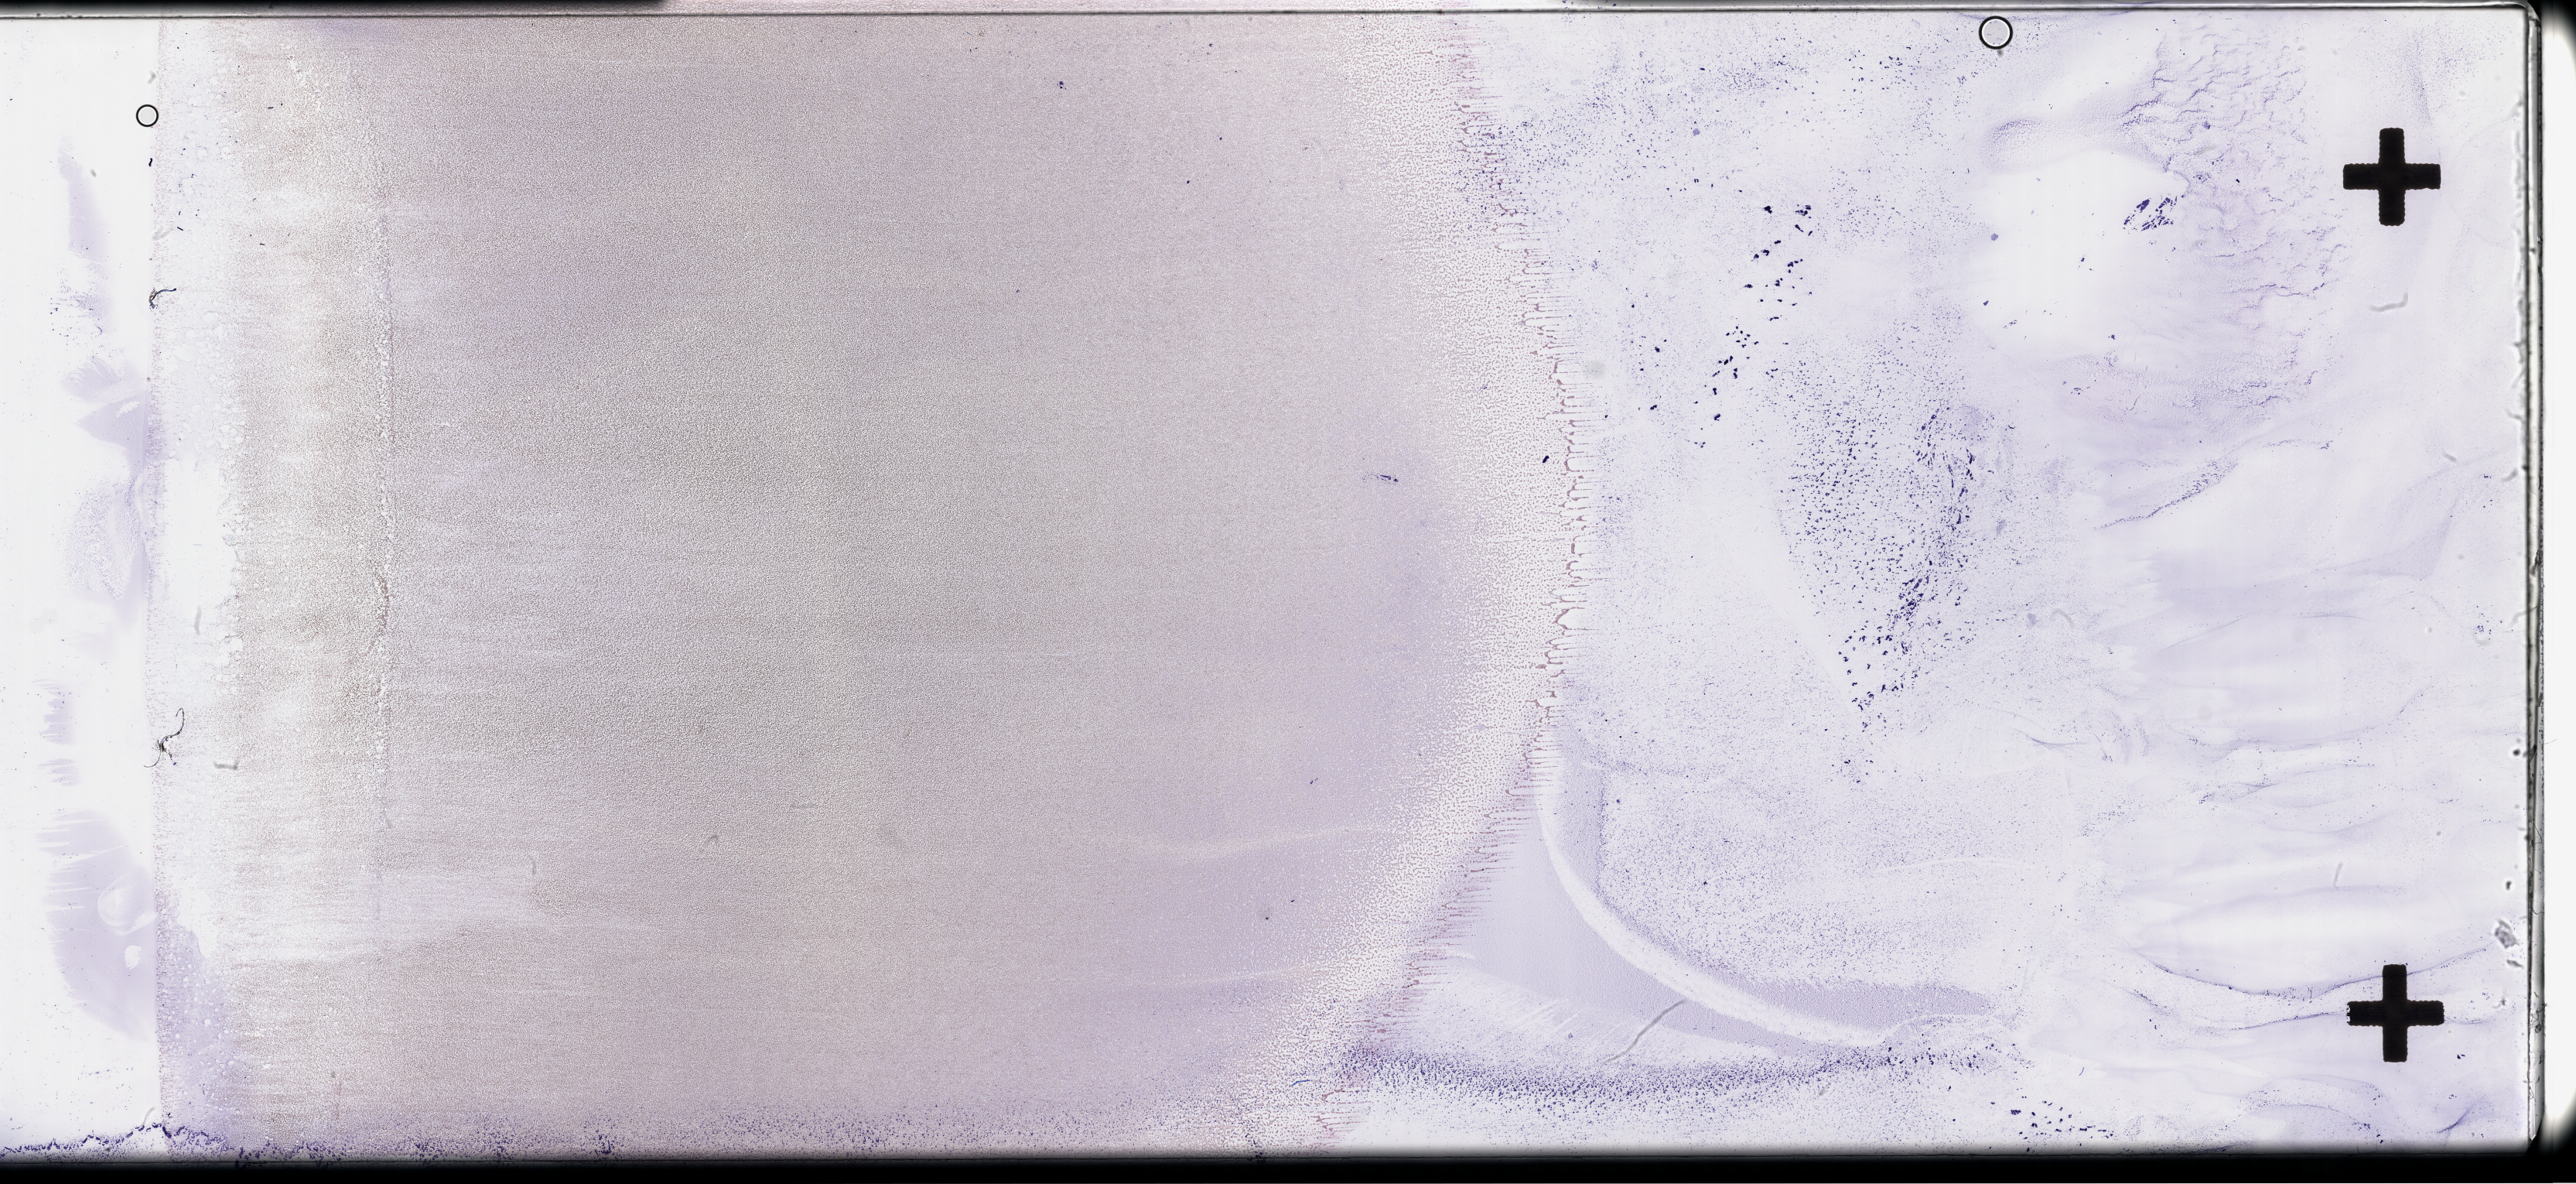
Whole-slide image of a whole blood smear, Wright-Giemsa stain — low-resolution overview of the scanned area, about 53.8 x 24.7 mm; EDTA-anticoagulated smear. Patient sex: female.
Patient diagnosis: Plasma Cell Myeloma.